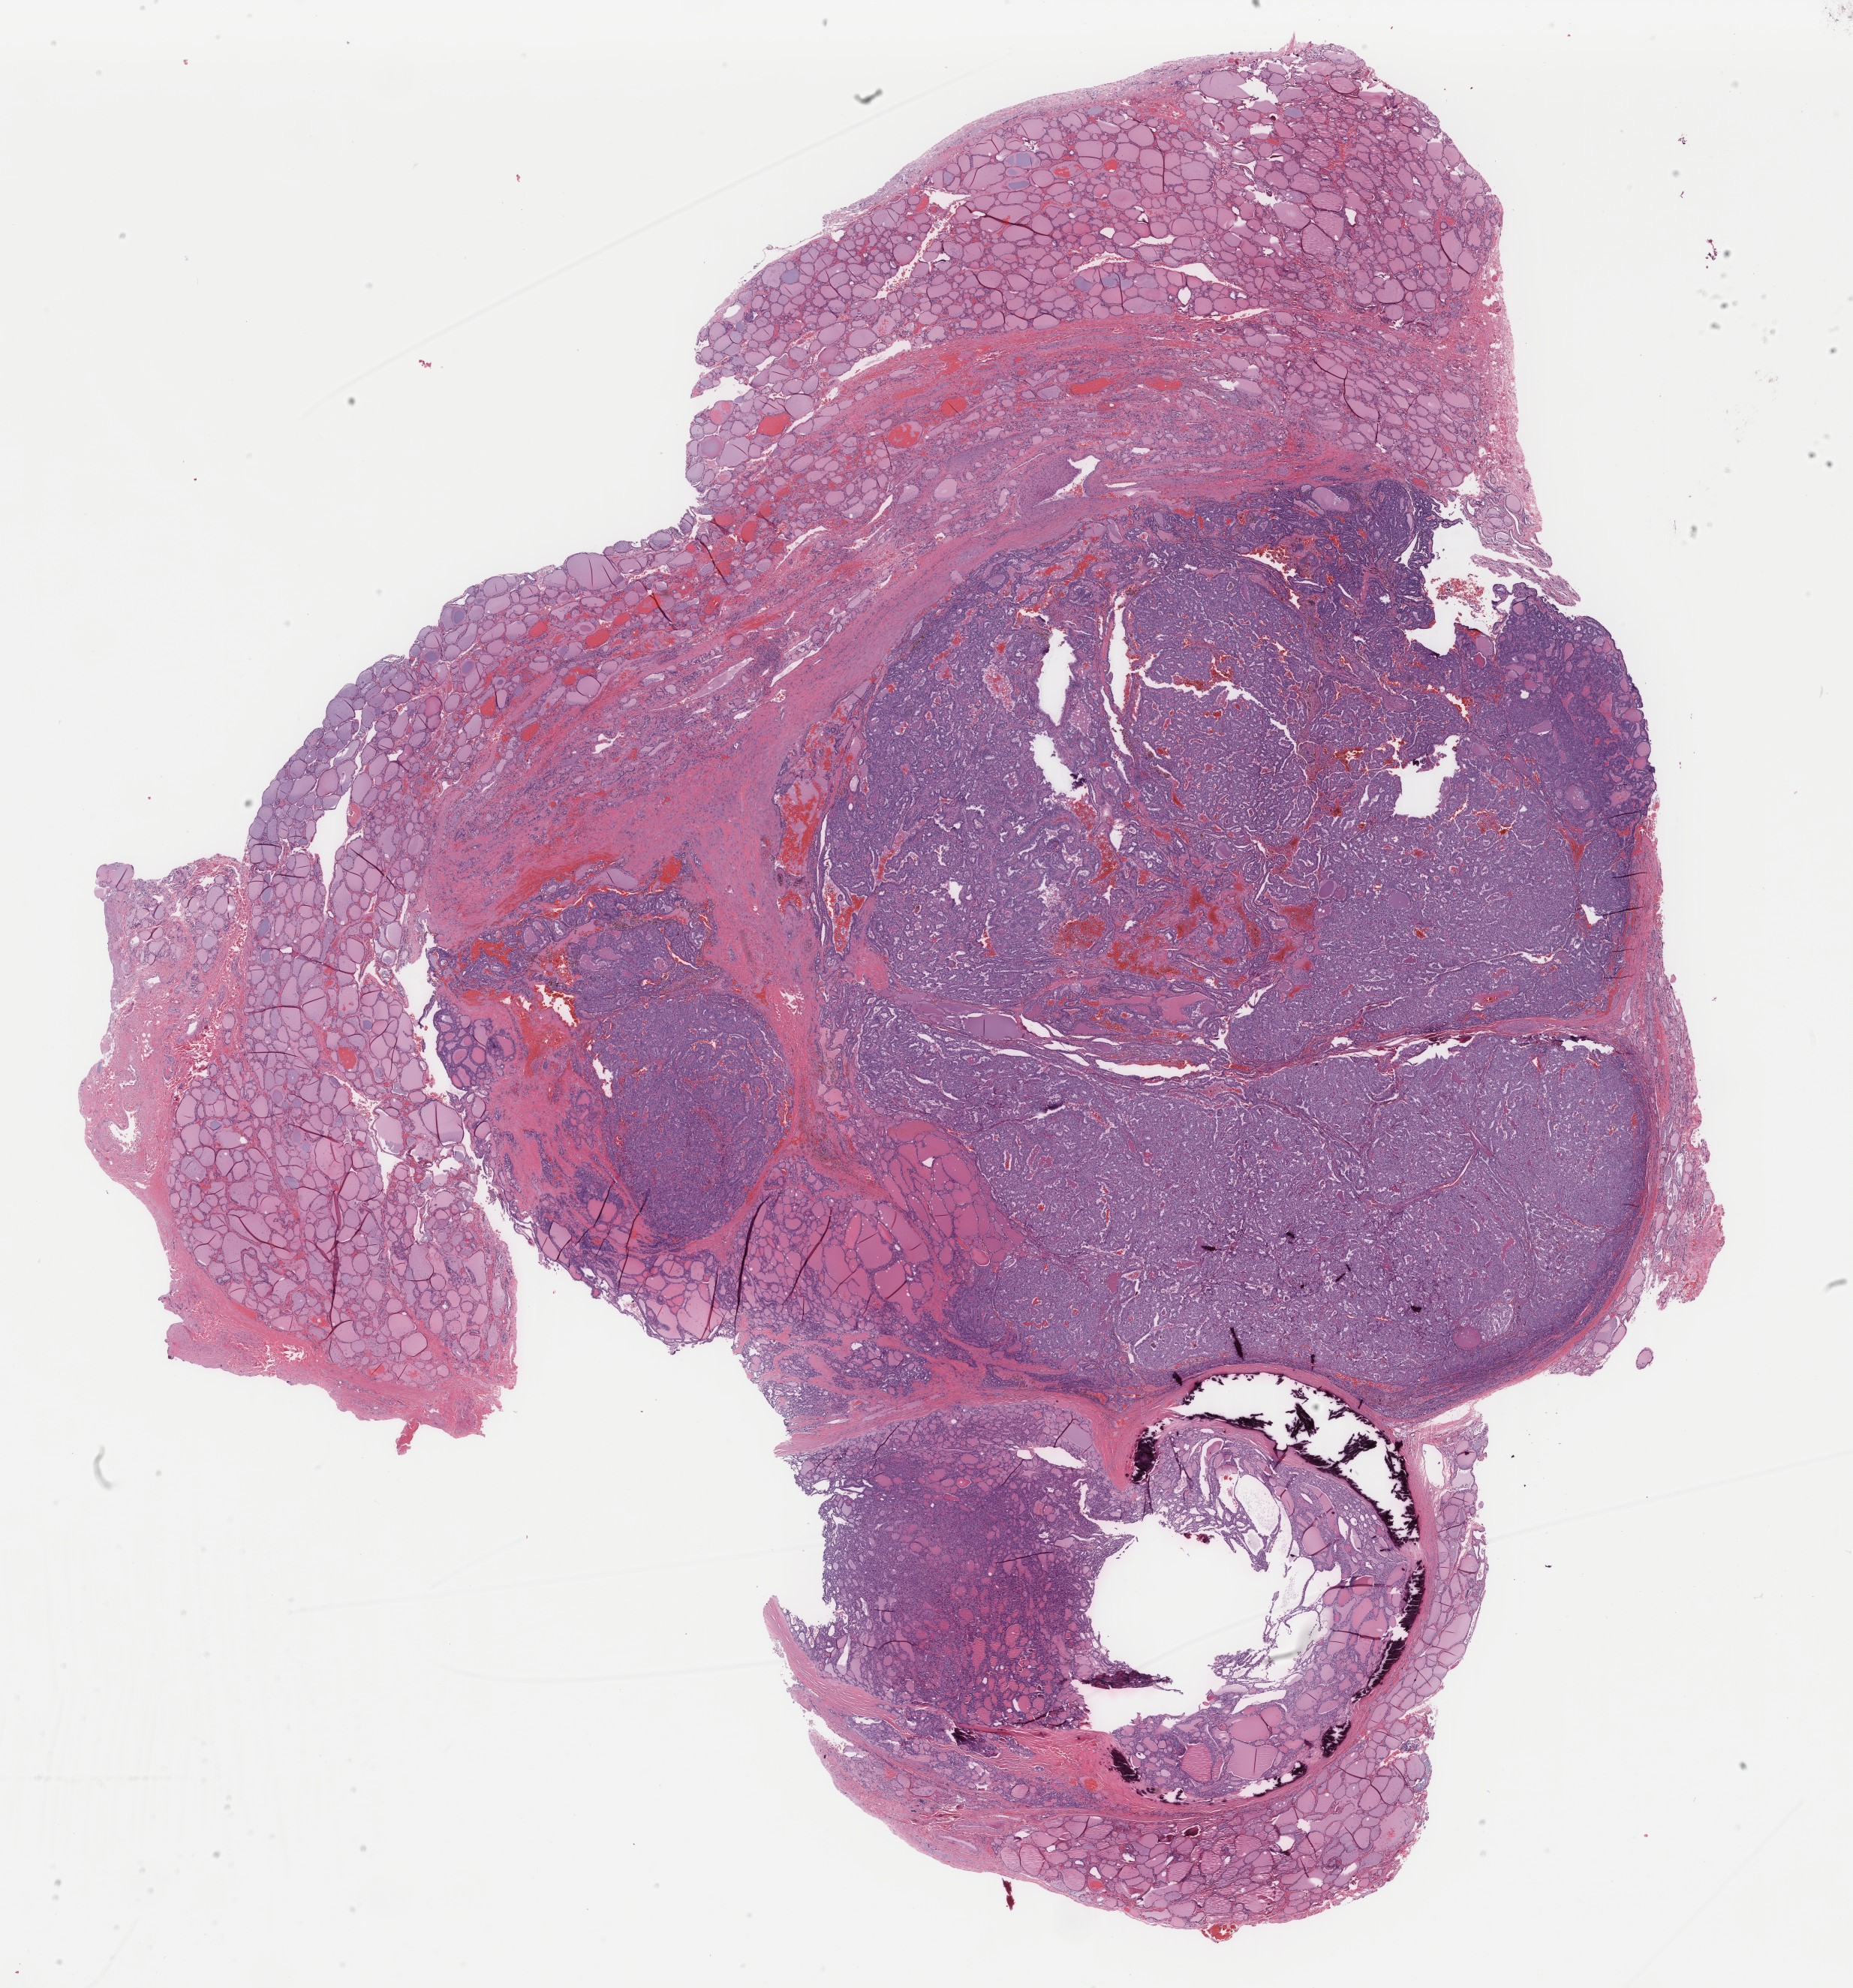
Digitized H&E tissue section (whole slide), shown as a low-resolution overview of the whole scanned area (about 19.6 x 21.0 mm, slide scanned at 40x). Formalin-fixed paraffin-embedded (FFPE) diagnostic section. Primary tumour sample from the thyroid. Female patient; age at initial diagnosis 37 years.
AJCC pathologic stage: I. Histologic diagnosis: Papillary adenocarcinoma, NOS (thyroid gland).